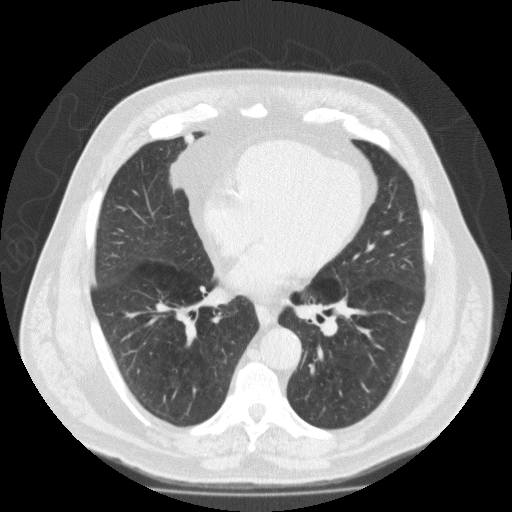
Low-dose screening chest CT, one axial slice. Lung window (W 1500 / L -600 HU). 2 mm slice thickness. 512 × 512 image matrix.
Outlined on this slice (outlined manually by an expert reader):
- lesion 1 (tumor, lower lobe of right lung): bounding box <170,134,201,189> (left, top, right, bottom; pixels)